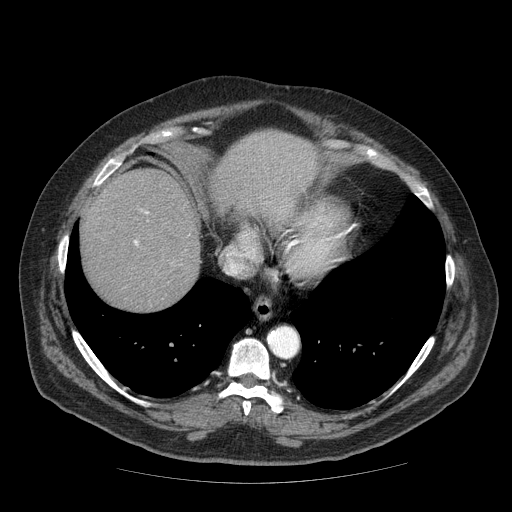
Contrast-enhanced abdominal CT (liver protocol), one axial slice. Position 62 of 85 along the scan axis. Reconstruction kernel STANDARD. Soft-tissue window (W 400 / L 40 HU). 2.5 mm slice thickness. 512 × 512 image matrix, field of view 420 × 420 mm. From the clinical record (not read from this slice): diagnosis: hepatocellular carcinoma (patient treated with transarterial chemoembolisation; whether this scan precedes or follows treatment is not stated here); TNM stage (as recorded): Stage-IIIA; Child-Pugh class: A; tumour size: 7 cm.
Outlined on this slice (semi-automatically segmented with operator editing):
- liver parenchyma outside the tumour (the mass and vessels are separate outlines, so this box may not span the whole liver): box from (x=80, y=132) to (x=316, y=310) px
- liver vessels: (x=134, y=241)–(x=138, y=245)